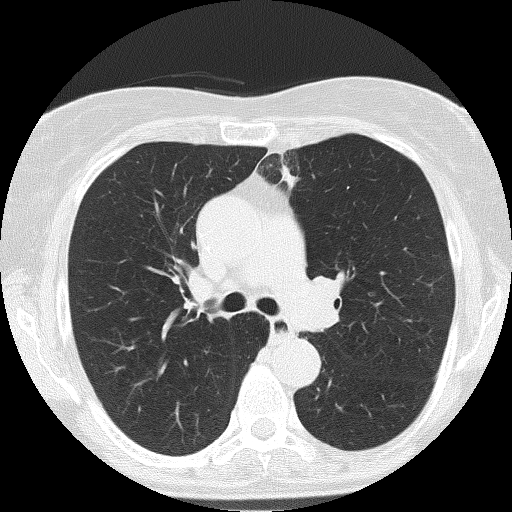
Low-dose screening chest CT, one axial slice; position 111 of 166 along the scan axis; reconstruction kernel FC51; 120 kVp; lung window (W 1500 / L -600 HU); 512 × 512 image matrix.
Structures marked on this image (outlined manually by an expert reader):
- lesion 2 (nodule, upper lobe of left lung): bounding box <282,166,296,185> (left, top, right, bottom; pixels)